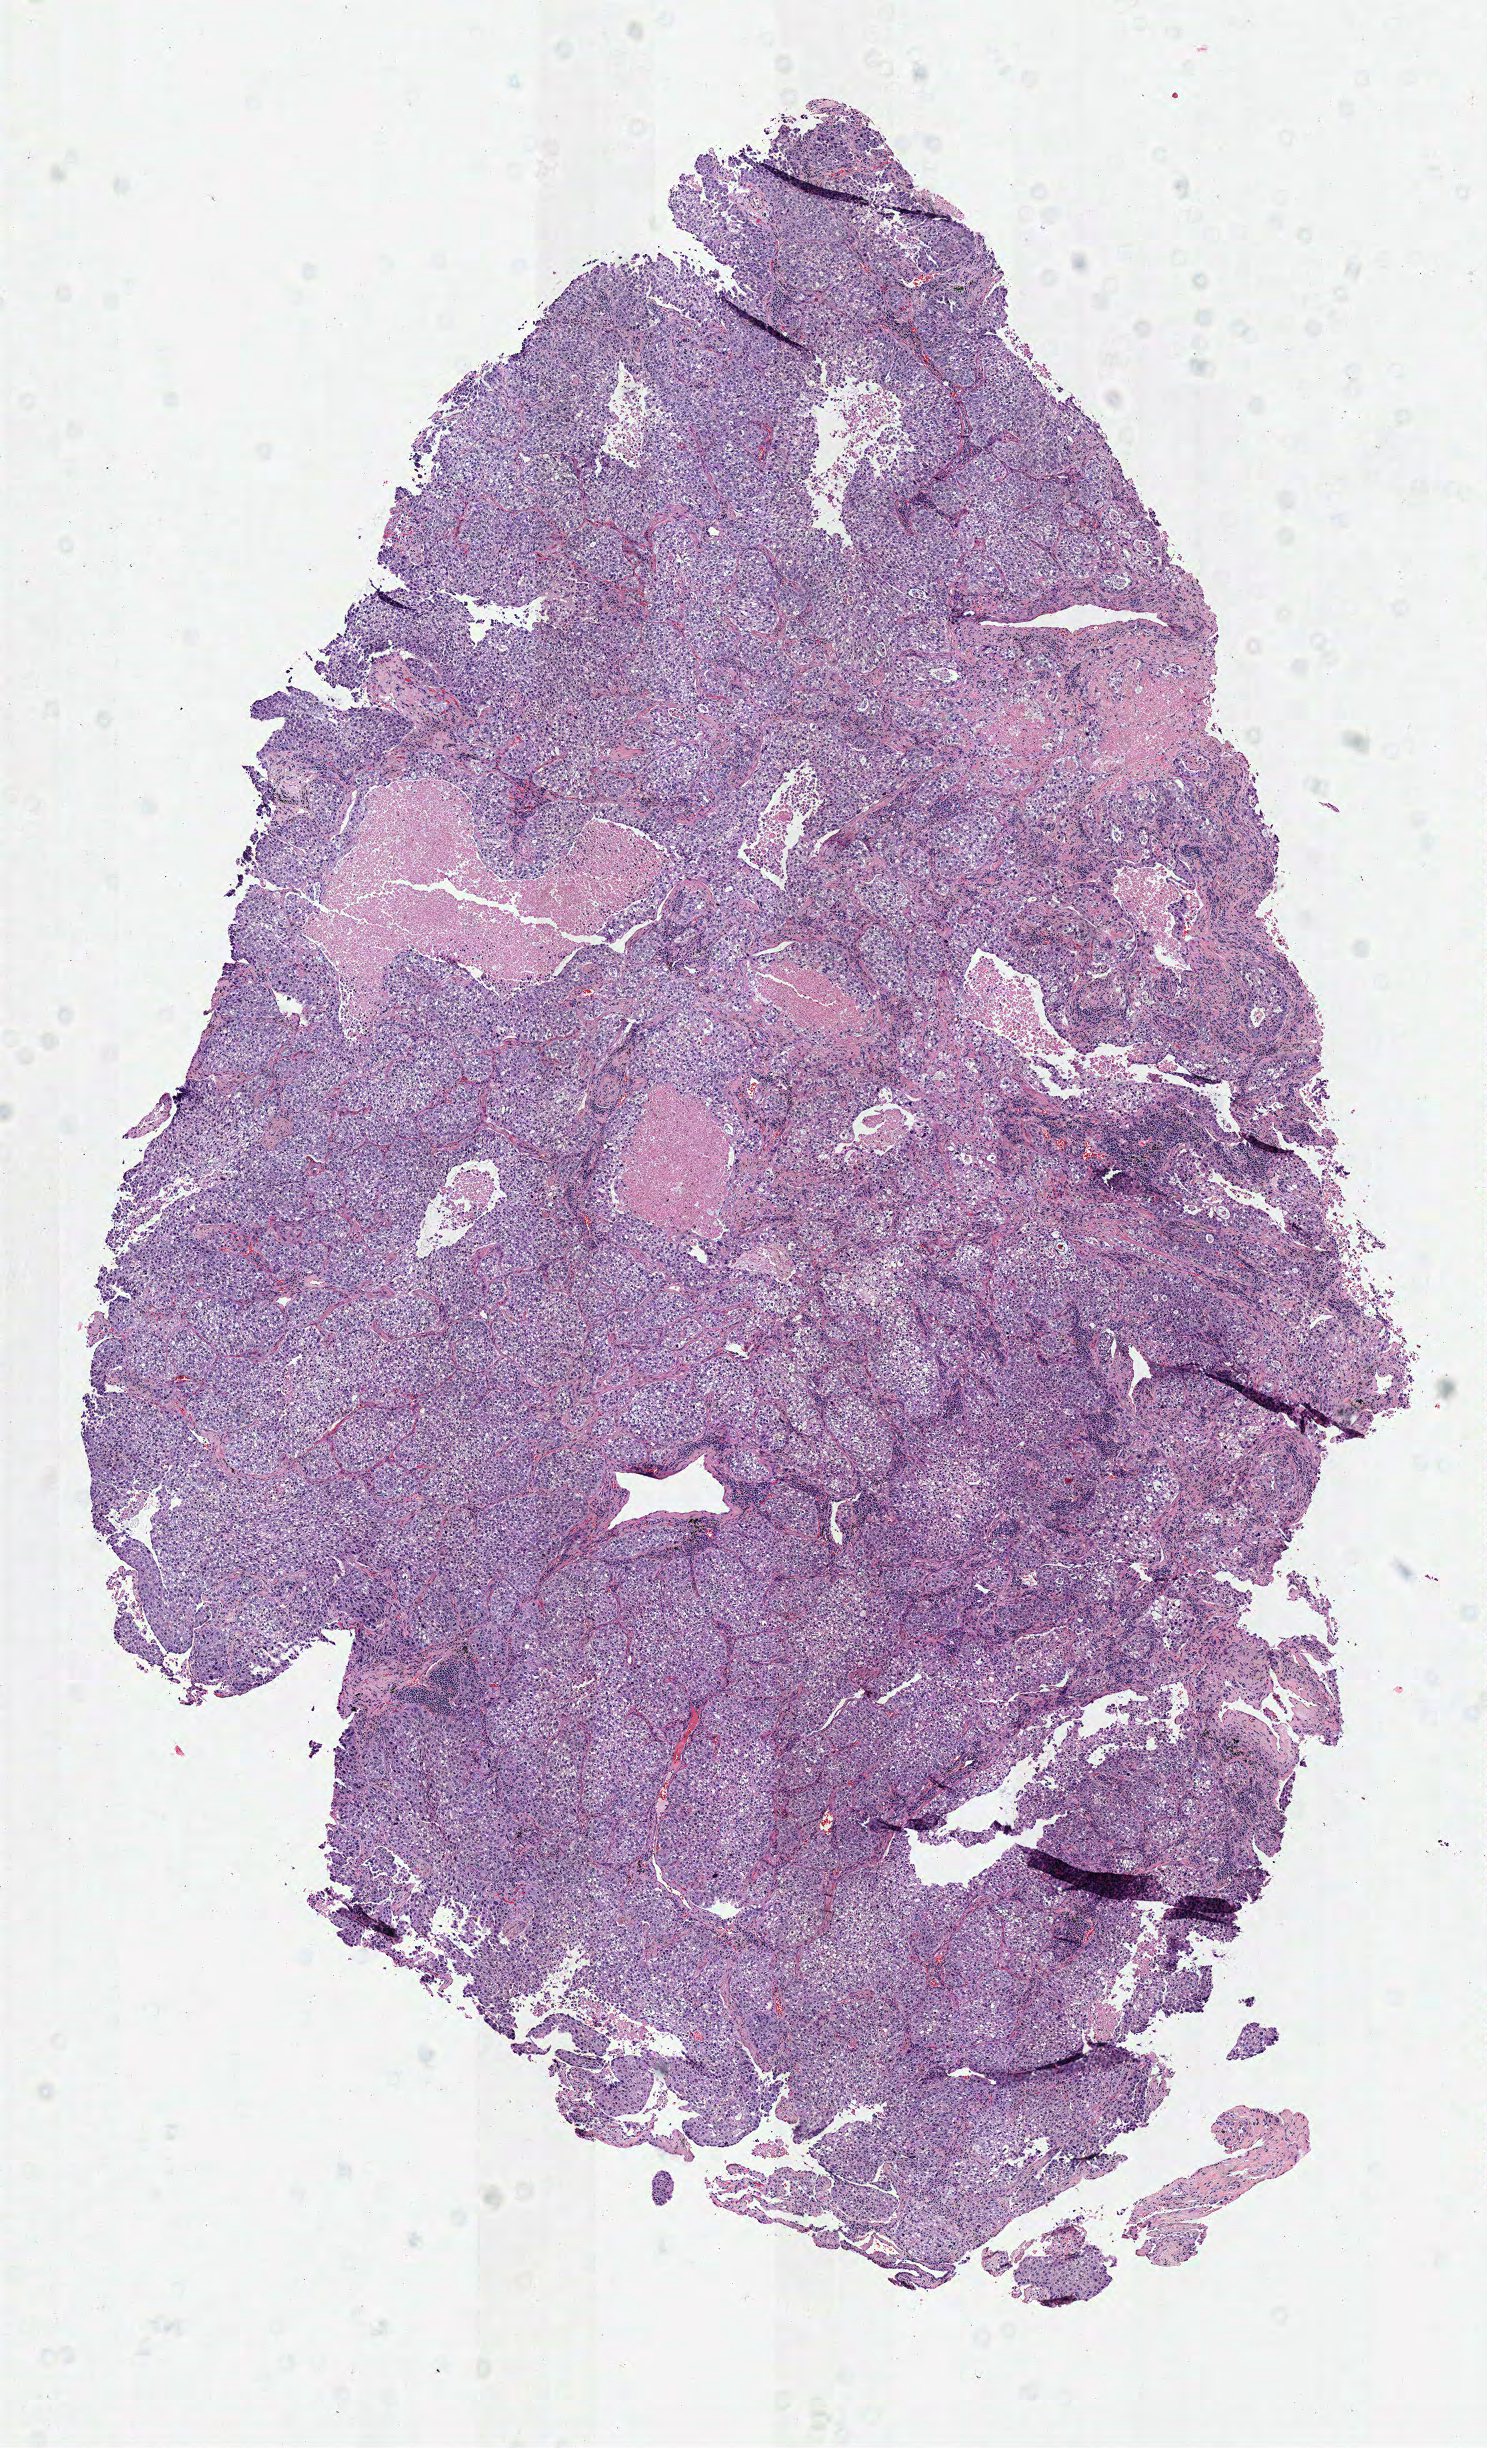
Whole-slide histology image, H&E-stained, shown as a low-resolution overview of the whole scanned area (about 5.9 x 9.6 mm, acquisition: 40x scan), frozen section from the top of the tissue portion, lung, primary tumour sample. Female, age 65 years at initial diagnosis. Composition of this section per pathologist review: tumour cells 83%, tumour nuclei 80%, normal cells 0%, stromal cells 5%, necrosis 12%.
• TNM: T1 N1 MX
• laterality: left
• AJCC pathologic stage: IIA (5th edition)
• histologic diagnosis: Adenocarcinoma, NOS